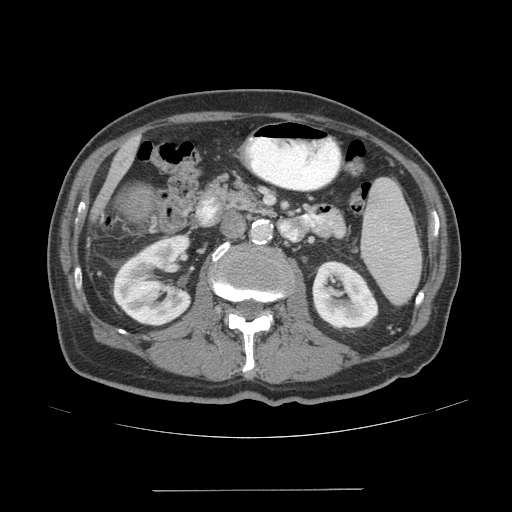
Contrast-enhanced abdominal CT (liver protocol), one axial slice; slice 8 of 77 in the series (ordered by position); reconstruction kernel STANDARD; 140 kVp; soft-tissue window (W 400 / L 40 HU); 2.5 mm slice thickness; 512 × 512 image matrix. Case-level facts recorded for this patient, not image findings: diagnosis: hepatocellular carcinoma (patient treated with transarterial chemoembolisation; whether this scan precedes or follows treatment is not stated here); TNM stage (as recorded): Stage-IVA; Child-Pugh class: A; tumour differentiation: well differentiated; tumour nodularity: uninodular.
Structures marked on this image (semi-automatically segmented with operator editing):
- liver parenchyma outside the tumour (the mass and vessels are separate outlines, so this box may not span the whole liver): bounding box (x1, y1, x2, y2) in pixels: (92, 137, 138, 220)
- mass: (124, 188, 154, 218)